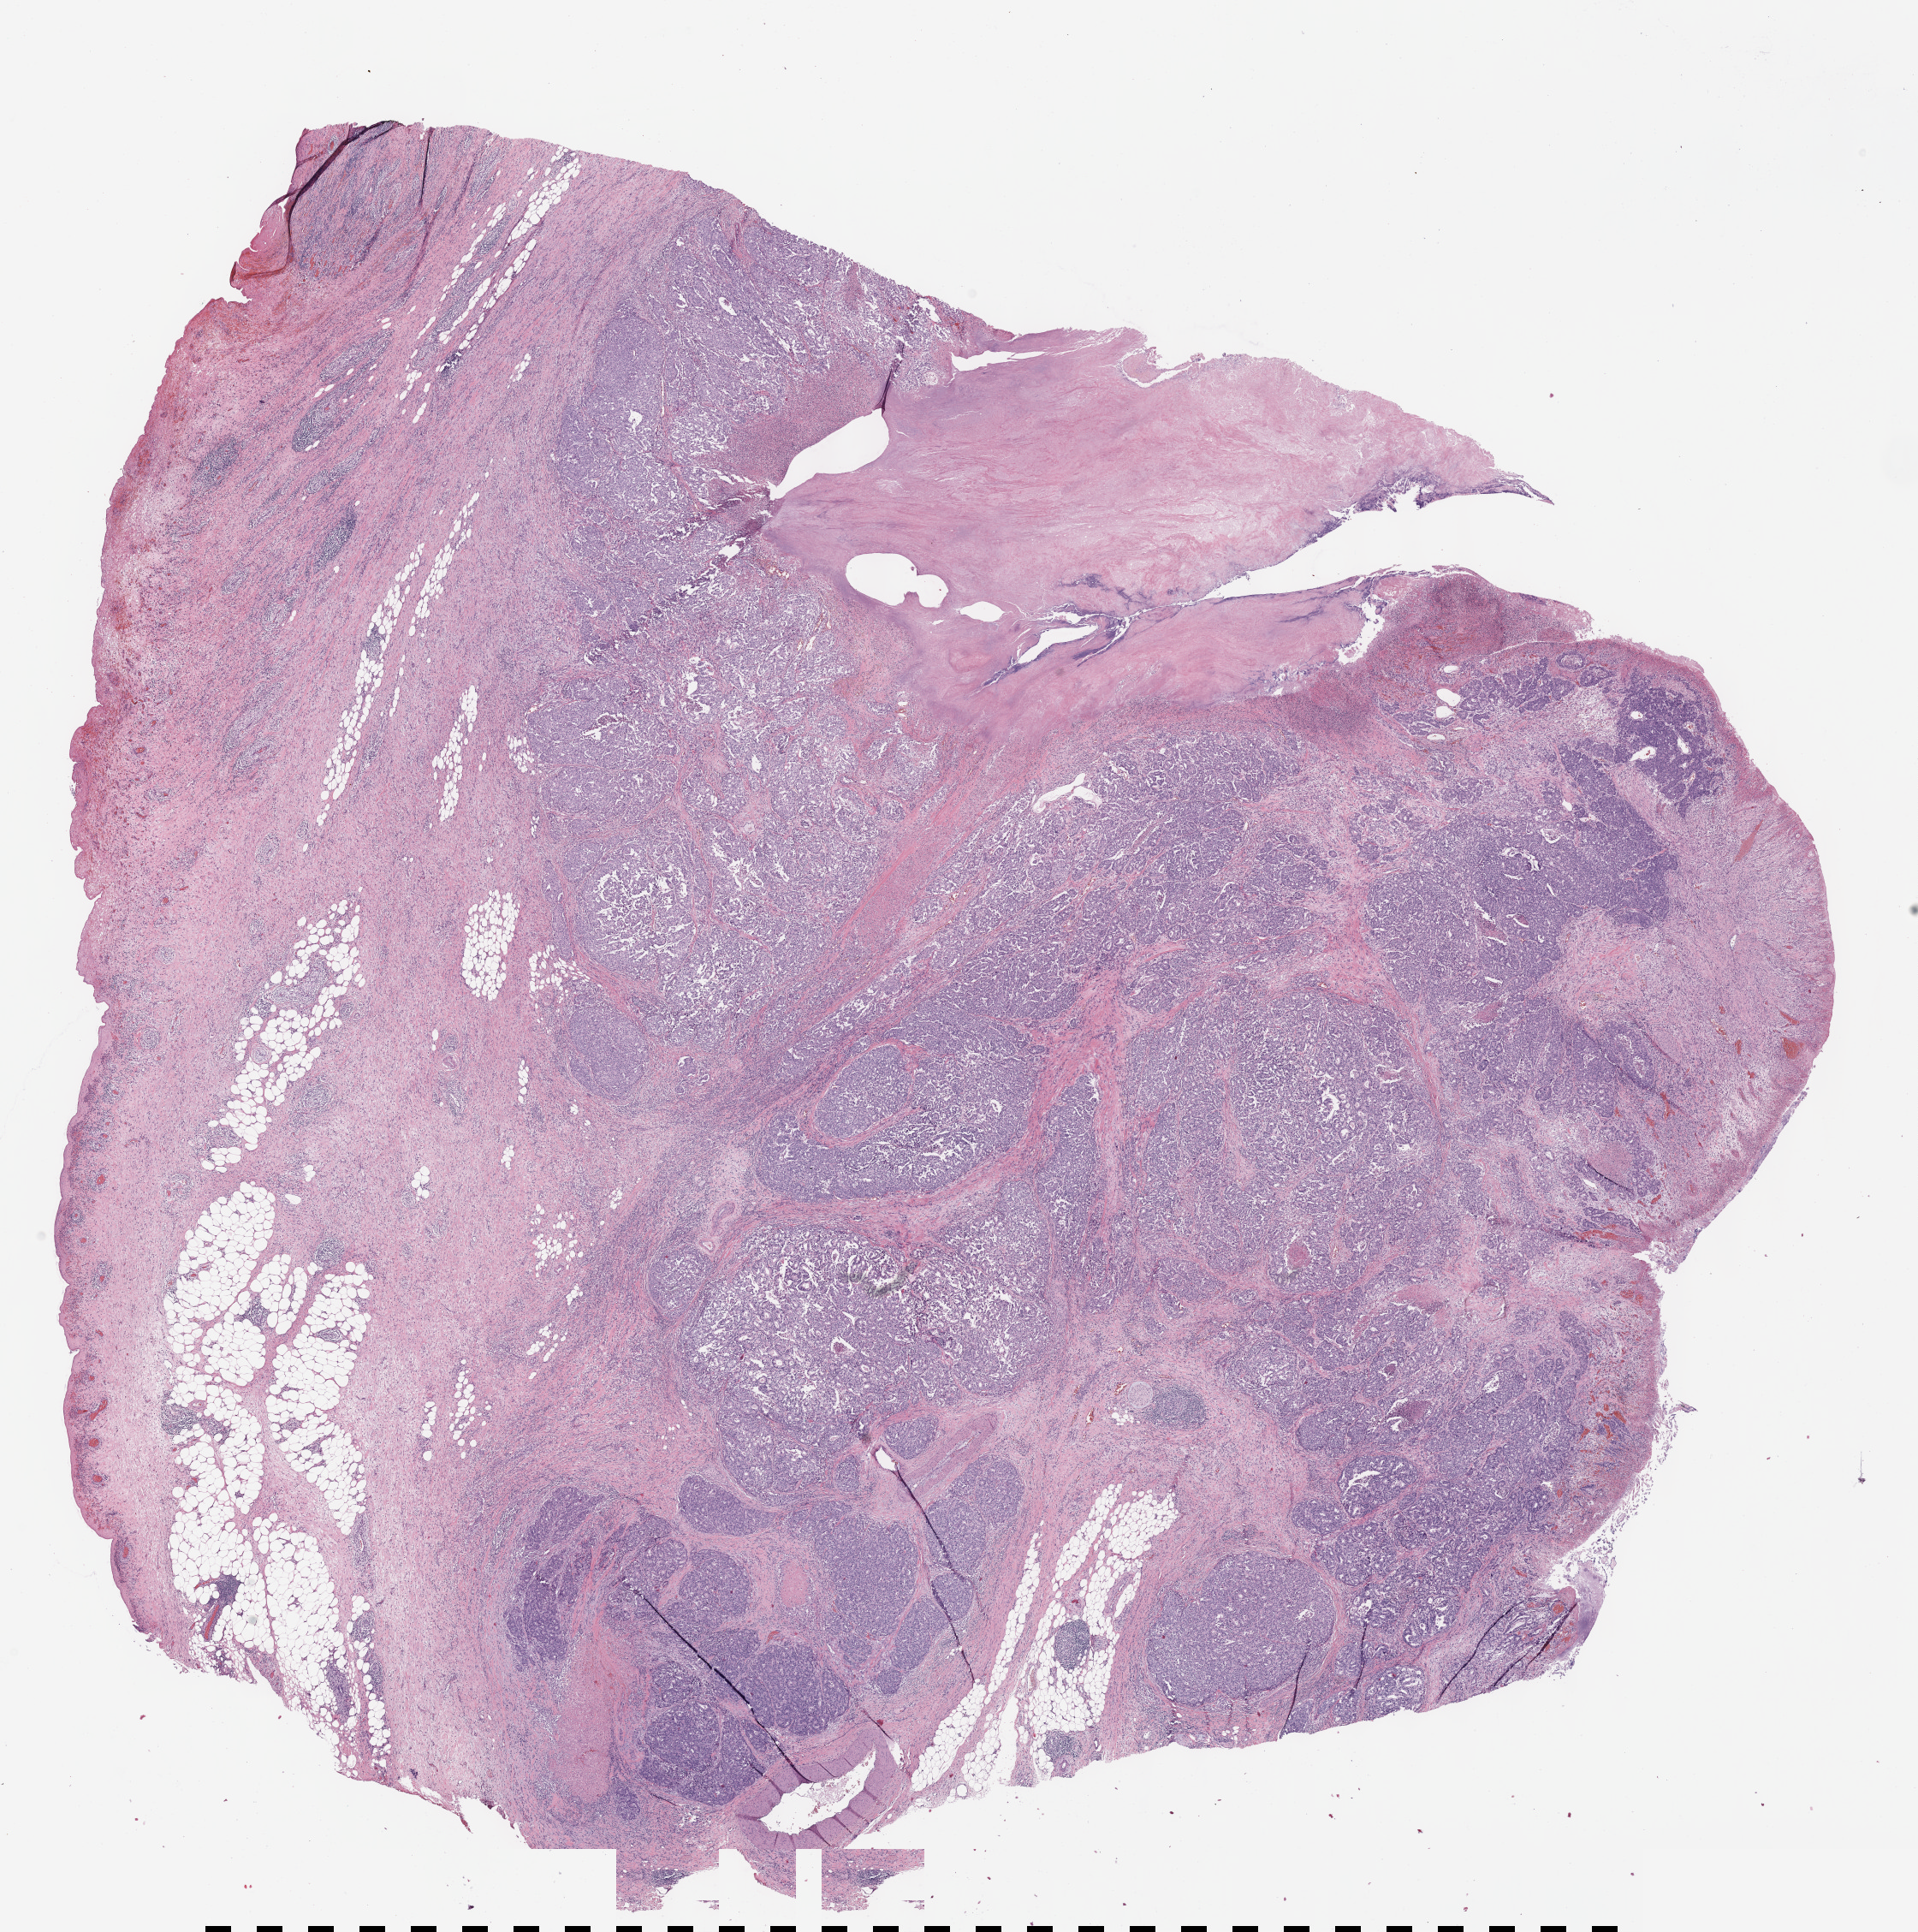
Digitized H&E tissue section (whole slide) — whole scanned area (about 18.1 x 18.2 mm) shown as a low-resolution overview; formalin-fixed paraffin-embedded (FFPE) diagnostic section; primary tumour sample from the stomach. Female, age 52 years at initial diagnosis.
Histologic diagnosis: Tubular adenocarcinoma (gastric antrum).